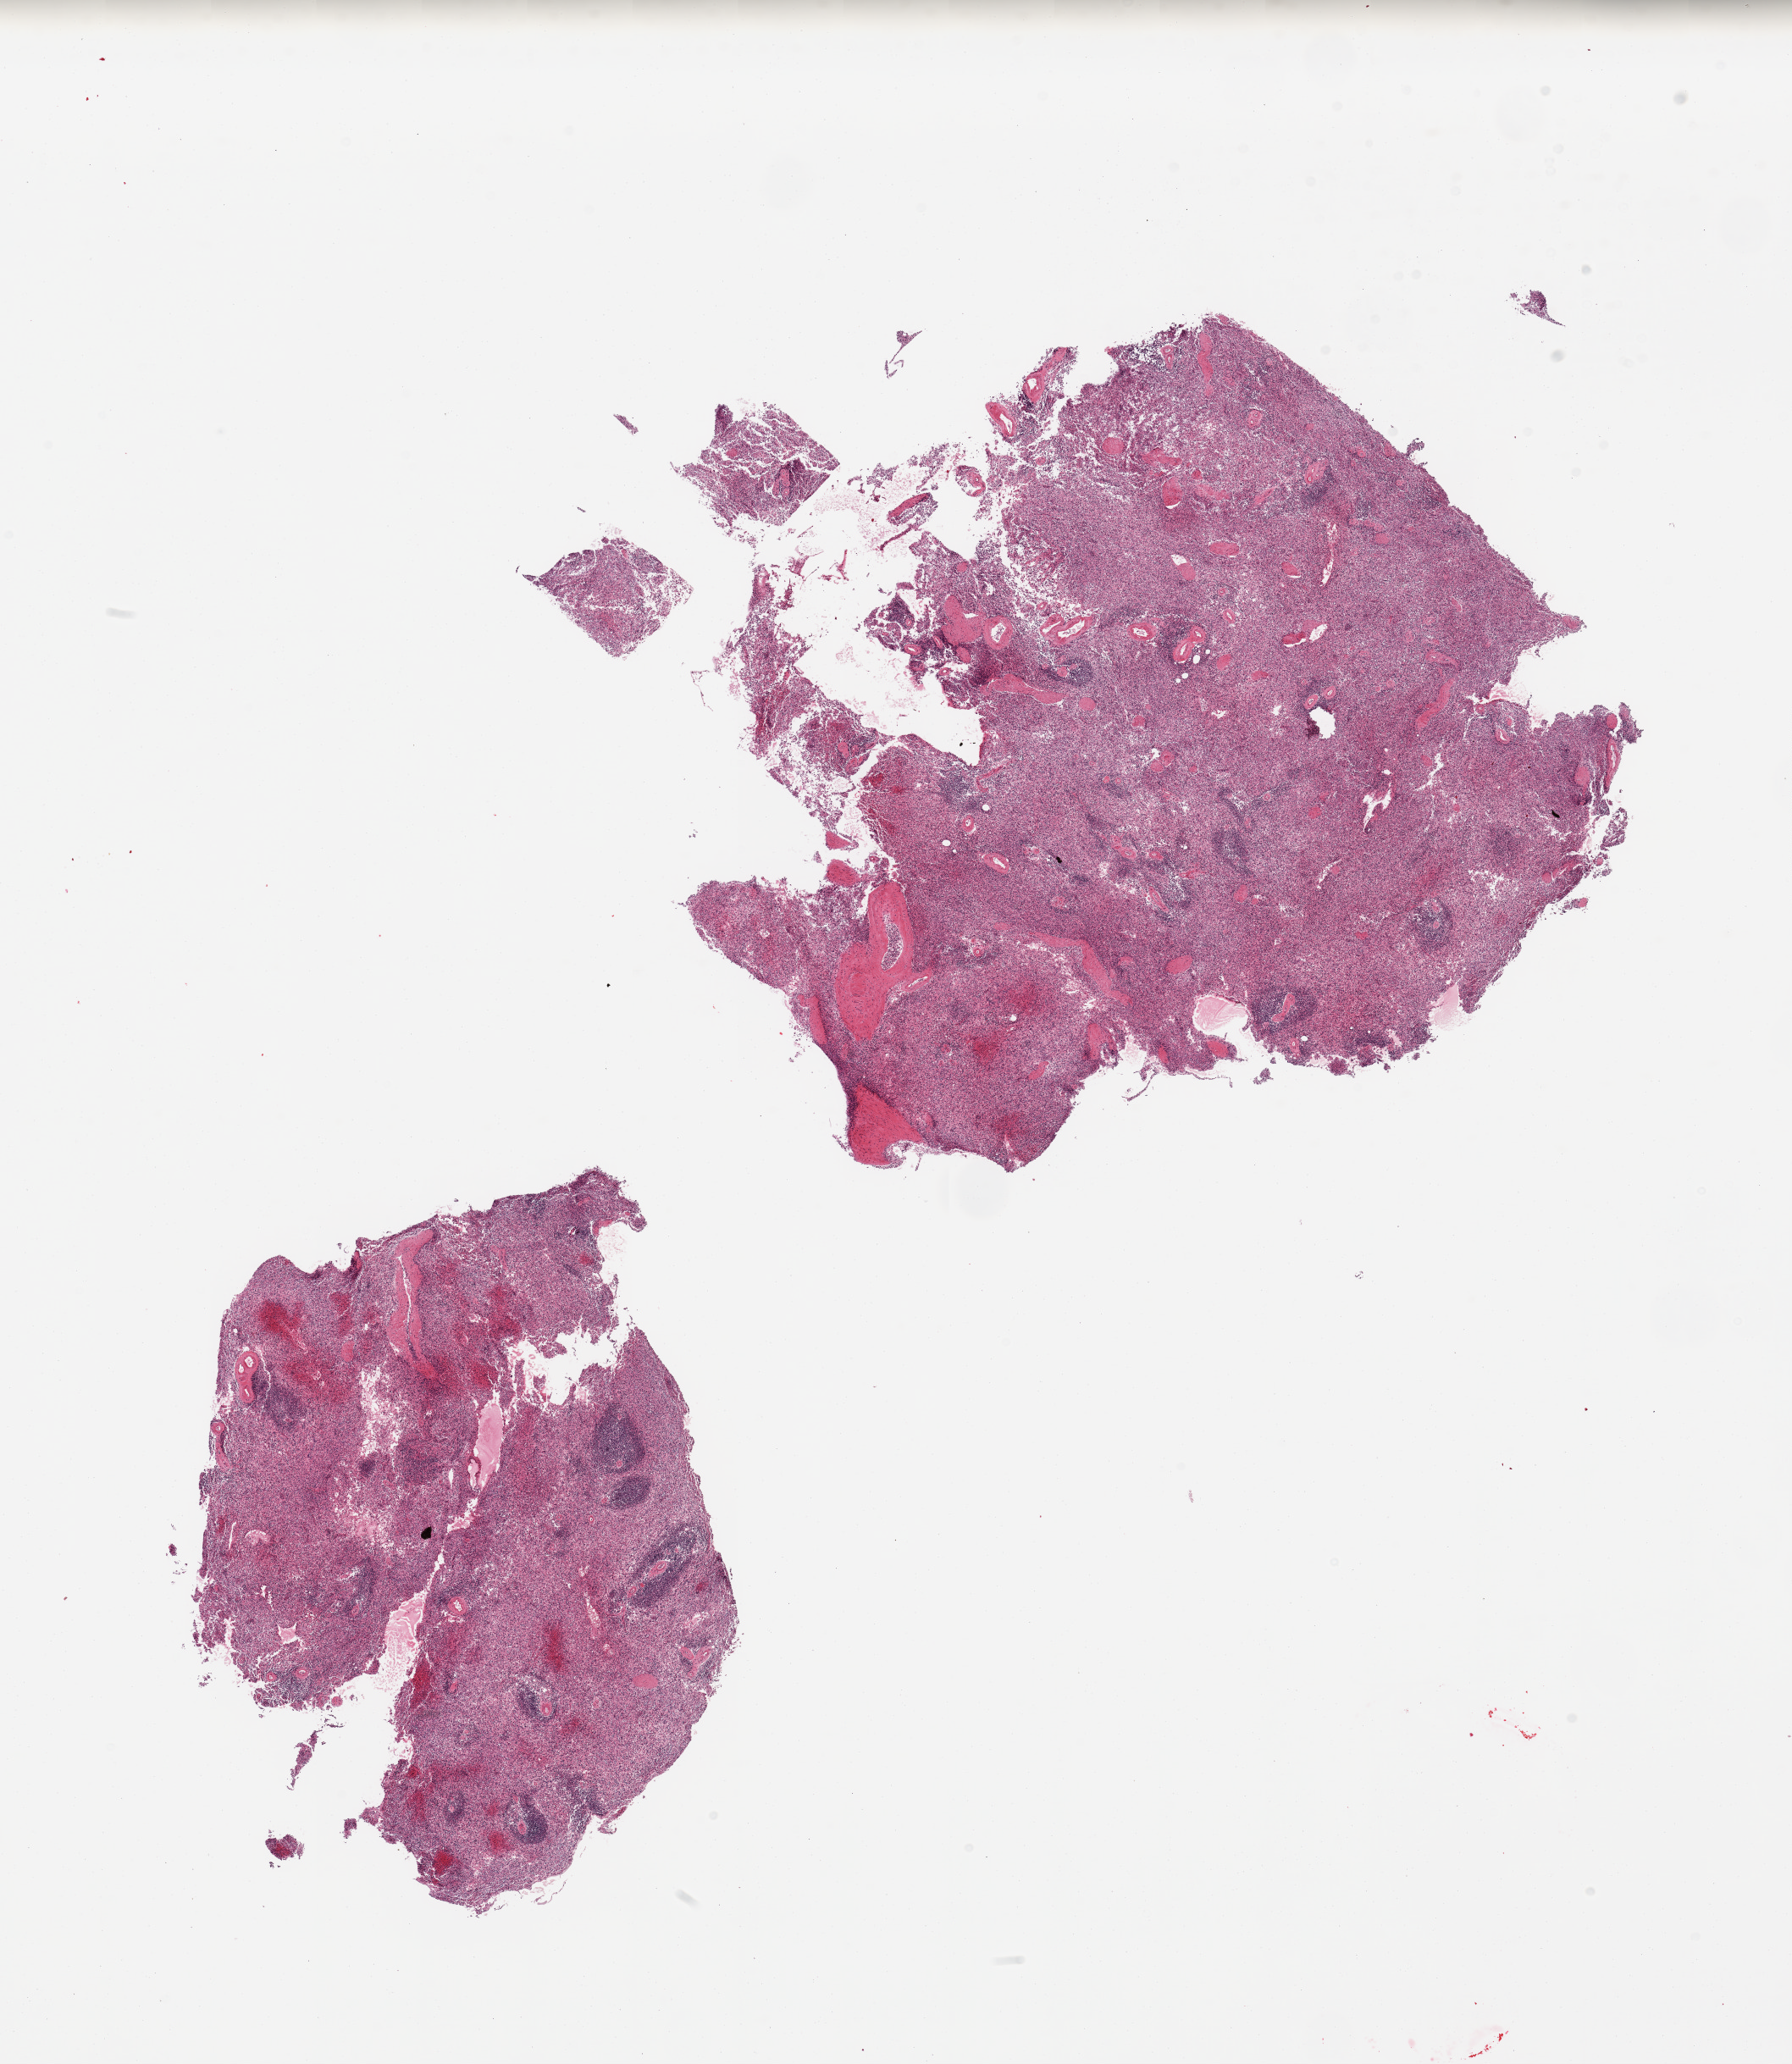
Digitized H&E-stained section, brightfield — whole scanned area (about 16.7 x 19.3 mm, acquisition: 20x scan) shown as a low-resolution overview; PAXgene-fixed paraffin-embedded (PFPE) section; sampled site (target tissue): spleen; donor tissue sample.
Reviewer comment on this tissue sample: 2 pieces, red pulp appears depleted.